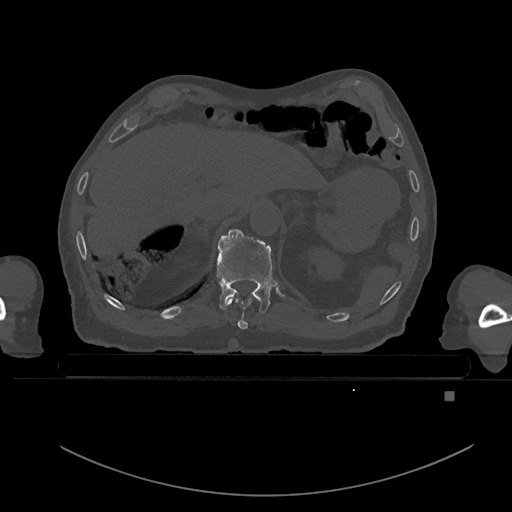
CT including the spine, one axial slice; slice 48 of 969 in the series (ordered by position); bone window (W 1800 / L 400 HU); 0.5 mm slice thickness; 512 × 512 image matrix, field of view 456 × 456 mm. Patient: male, 82 years. Case-level facts recorded for this patient, not image findings: primary cancer: prostate; vertebrae with lytic lesions (as recorded): T11, T9, T8, T2.
Outlined on this slice (semi-automatic segmentation, software-assisted and operator-edited):
- T10 vertebra: bounding box (x1, y1, x2, y2) in pixels: (227, 298, 253, 330)
- T11 vertebra: (216, 228, 277, 314)